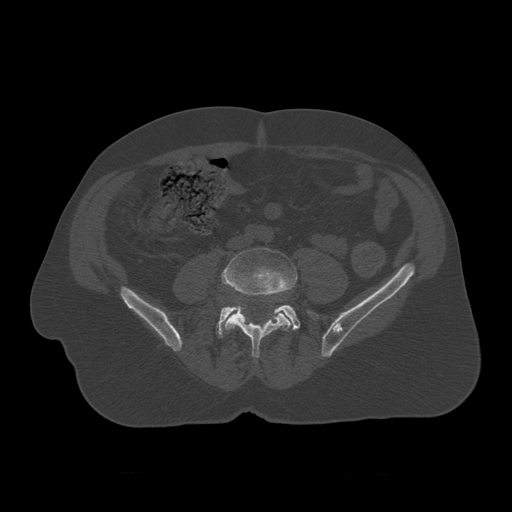
CT including the spine, one axial slice. 120 kVp. Bone window (W 1800 / L 400 HU). 1.25 mm slice thickness. 512 × 512 image matrix. Patient age 75 years. From the clinical record (not read from this slice): primary cancer: prostate.
Outlined on this slice (semi-automatically segmented with operator editing):
- L4 vertebra: box from (x=222, y=248) to (x=298, y=358) px
- L5 vertebra: (x=216, y=305)–(x=319, y=339)